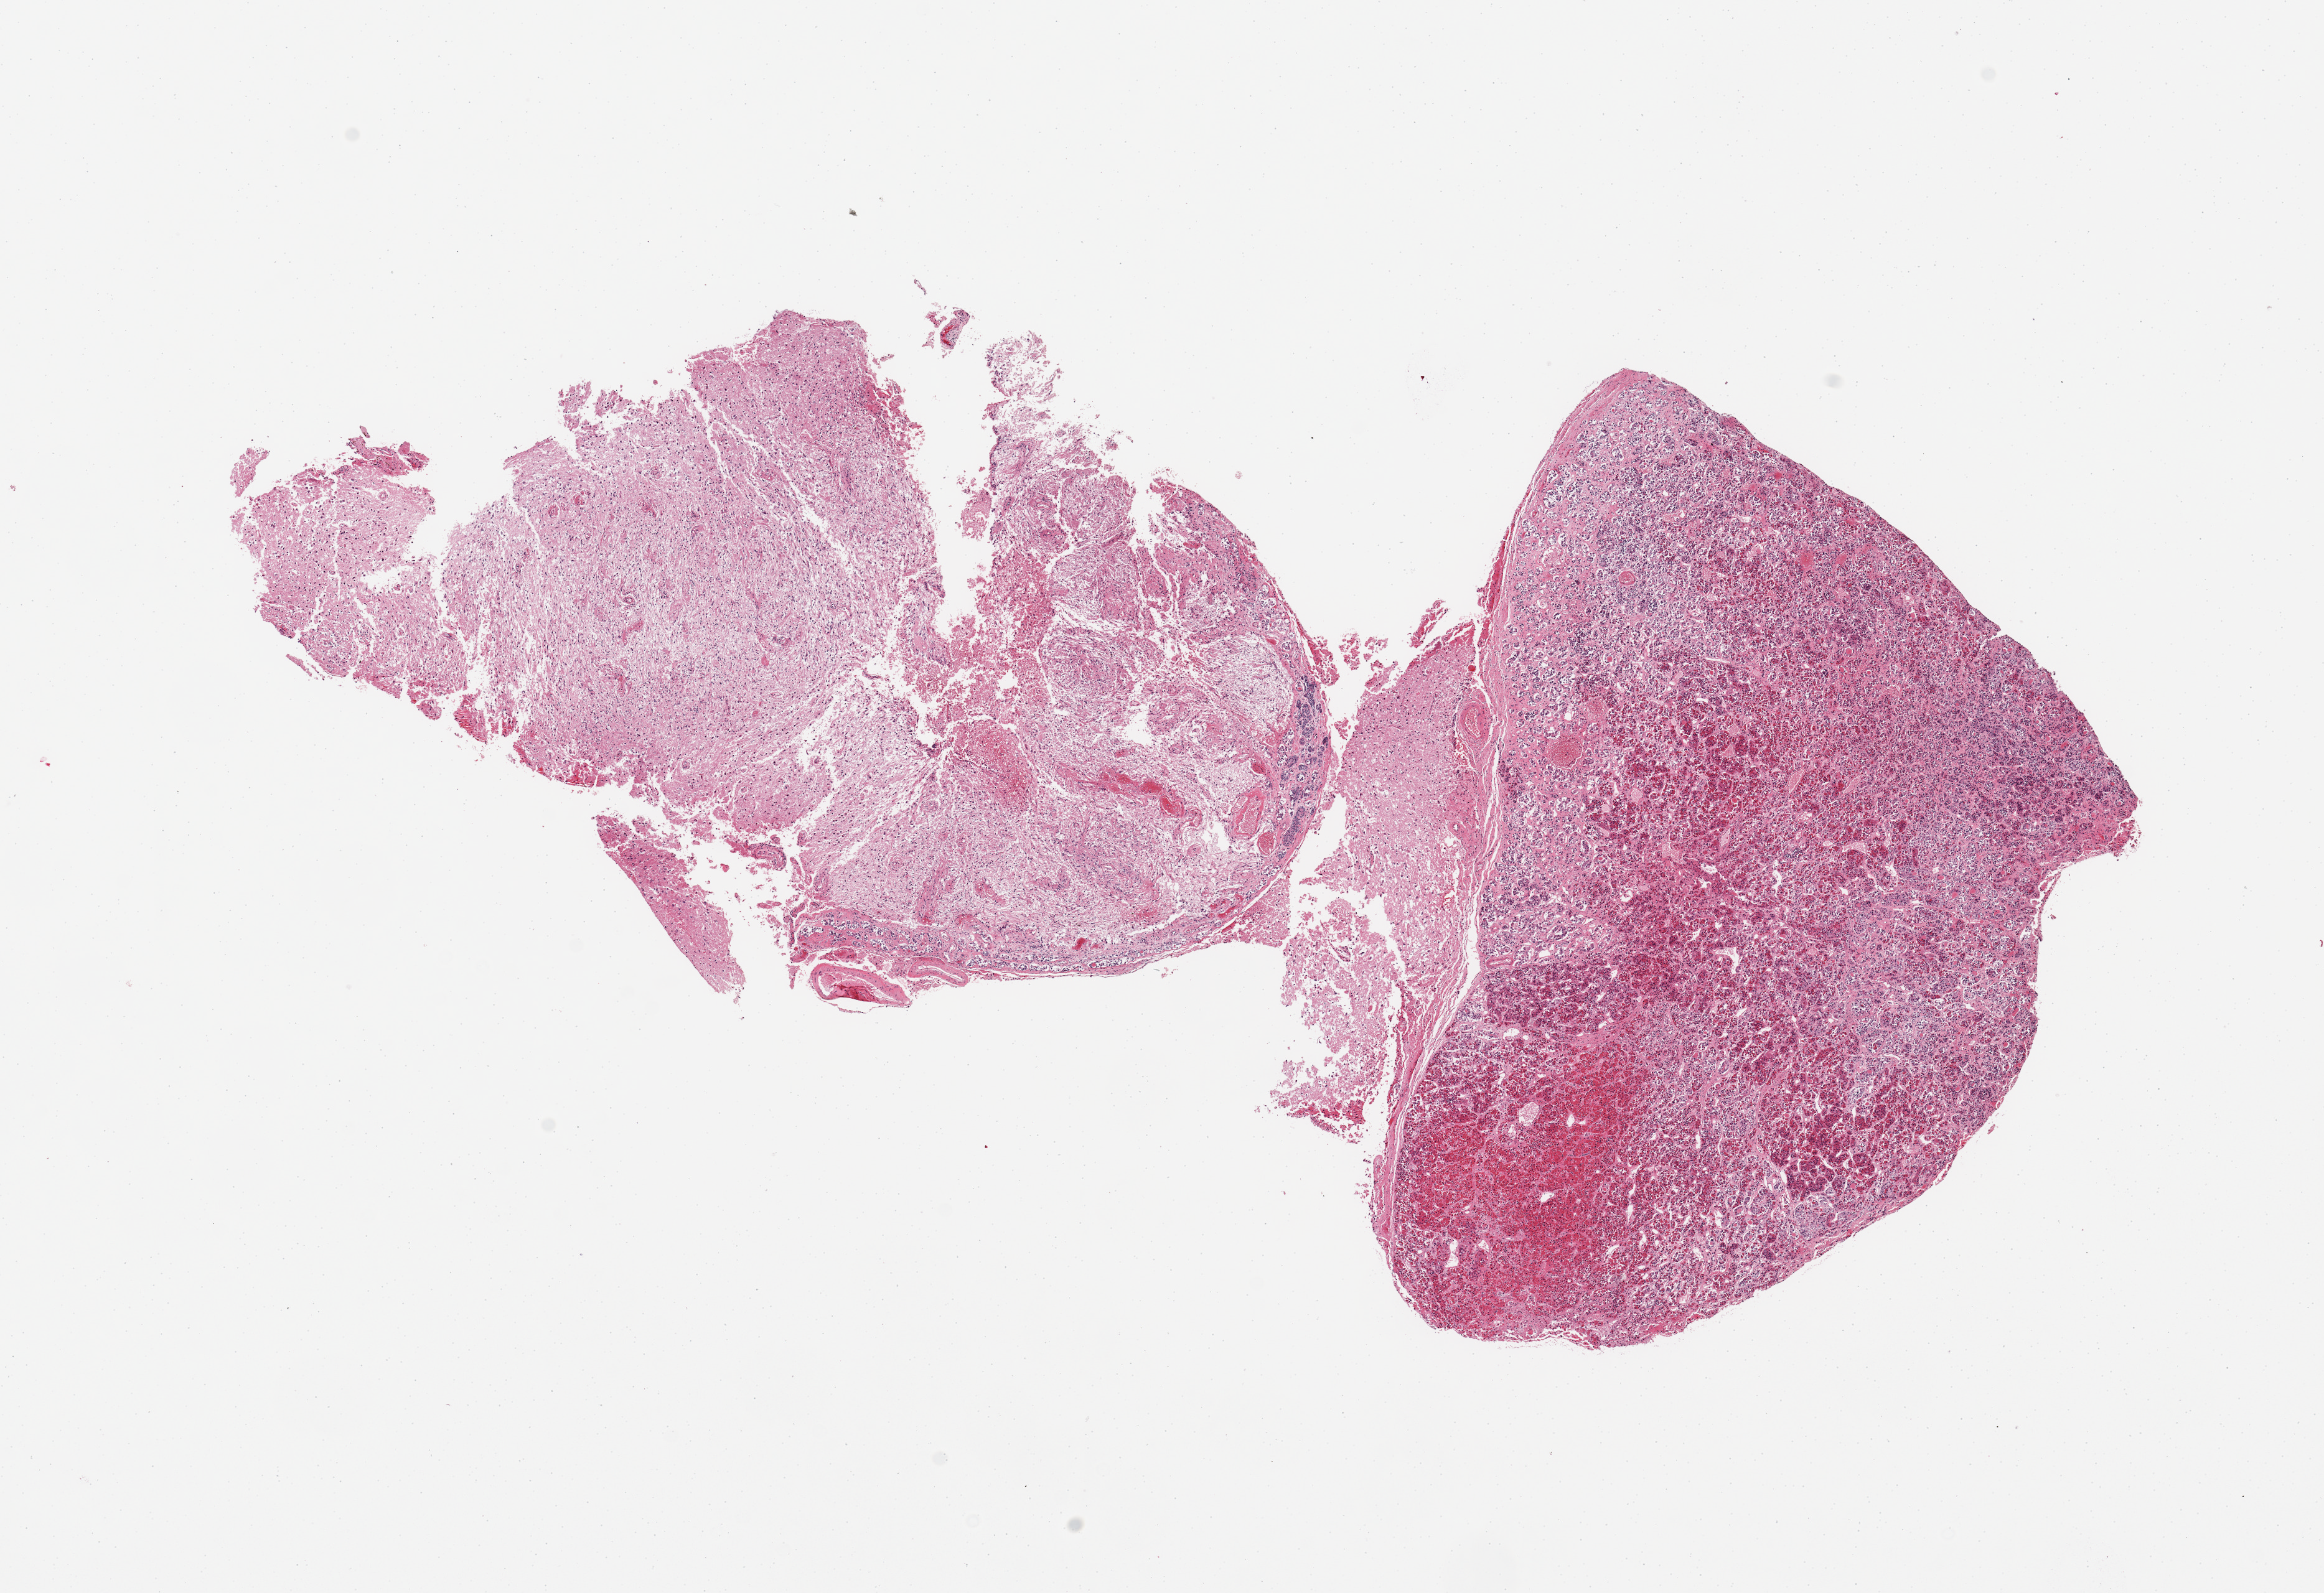
Haematoxylin and eosin whole-slide image, whole scanned area (about 14.8 x 10.1 mm, from a 20x scan) shown as a low-resolution overview, PAXgene-fixed, paraffin-embedded tissue, target tissue: pituitary, tissue donor sample.
Reviewer comment on this tissue sample: 2 pieces, 50% neurohypophysis; rest adenohypophysis.